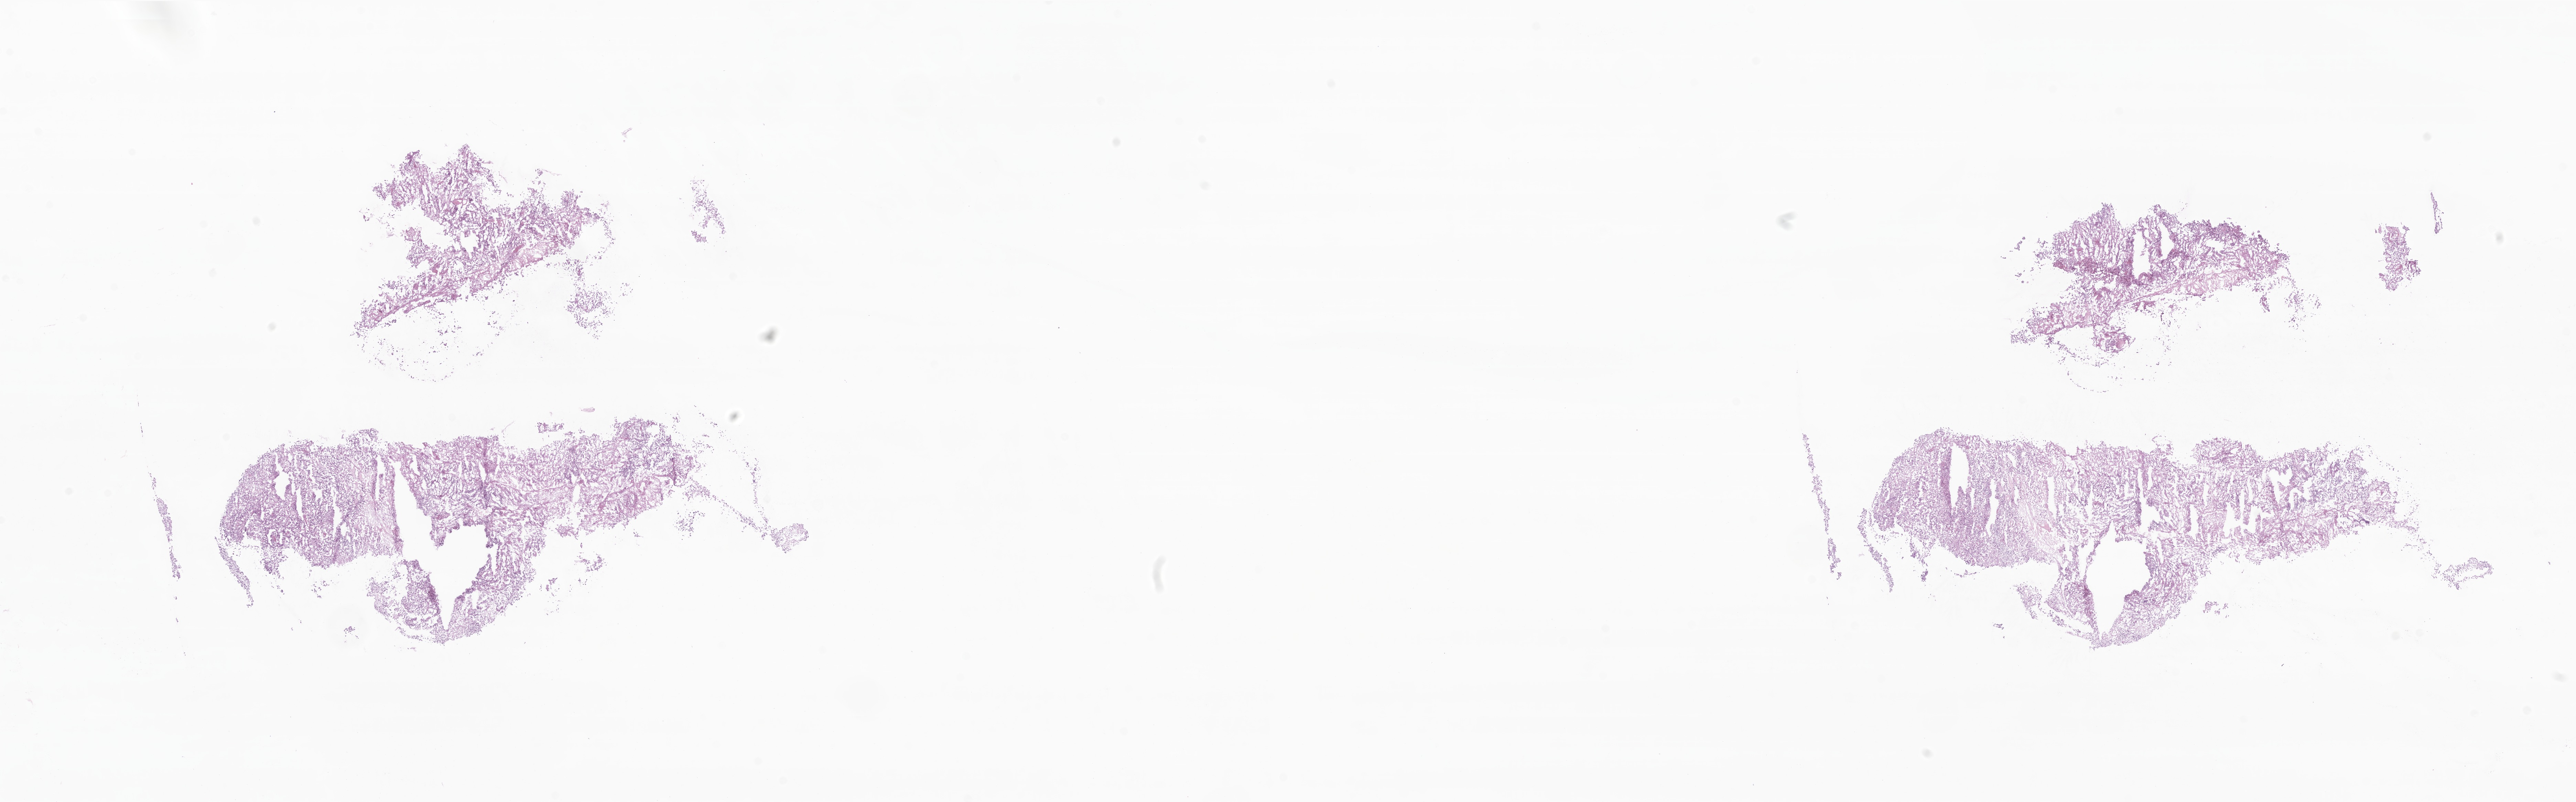
Hematoxylin and eosin (H&E) whole-slide image of tumor tissue from the brain, whole scanned area (about 31.6 x 9.8 mm) shown as a low-resolution overview; frozen section (OCT-embedded). Patient female; age 153 months (12 years 9 months).
- diagnosis: Glioma, malignant